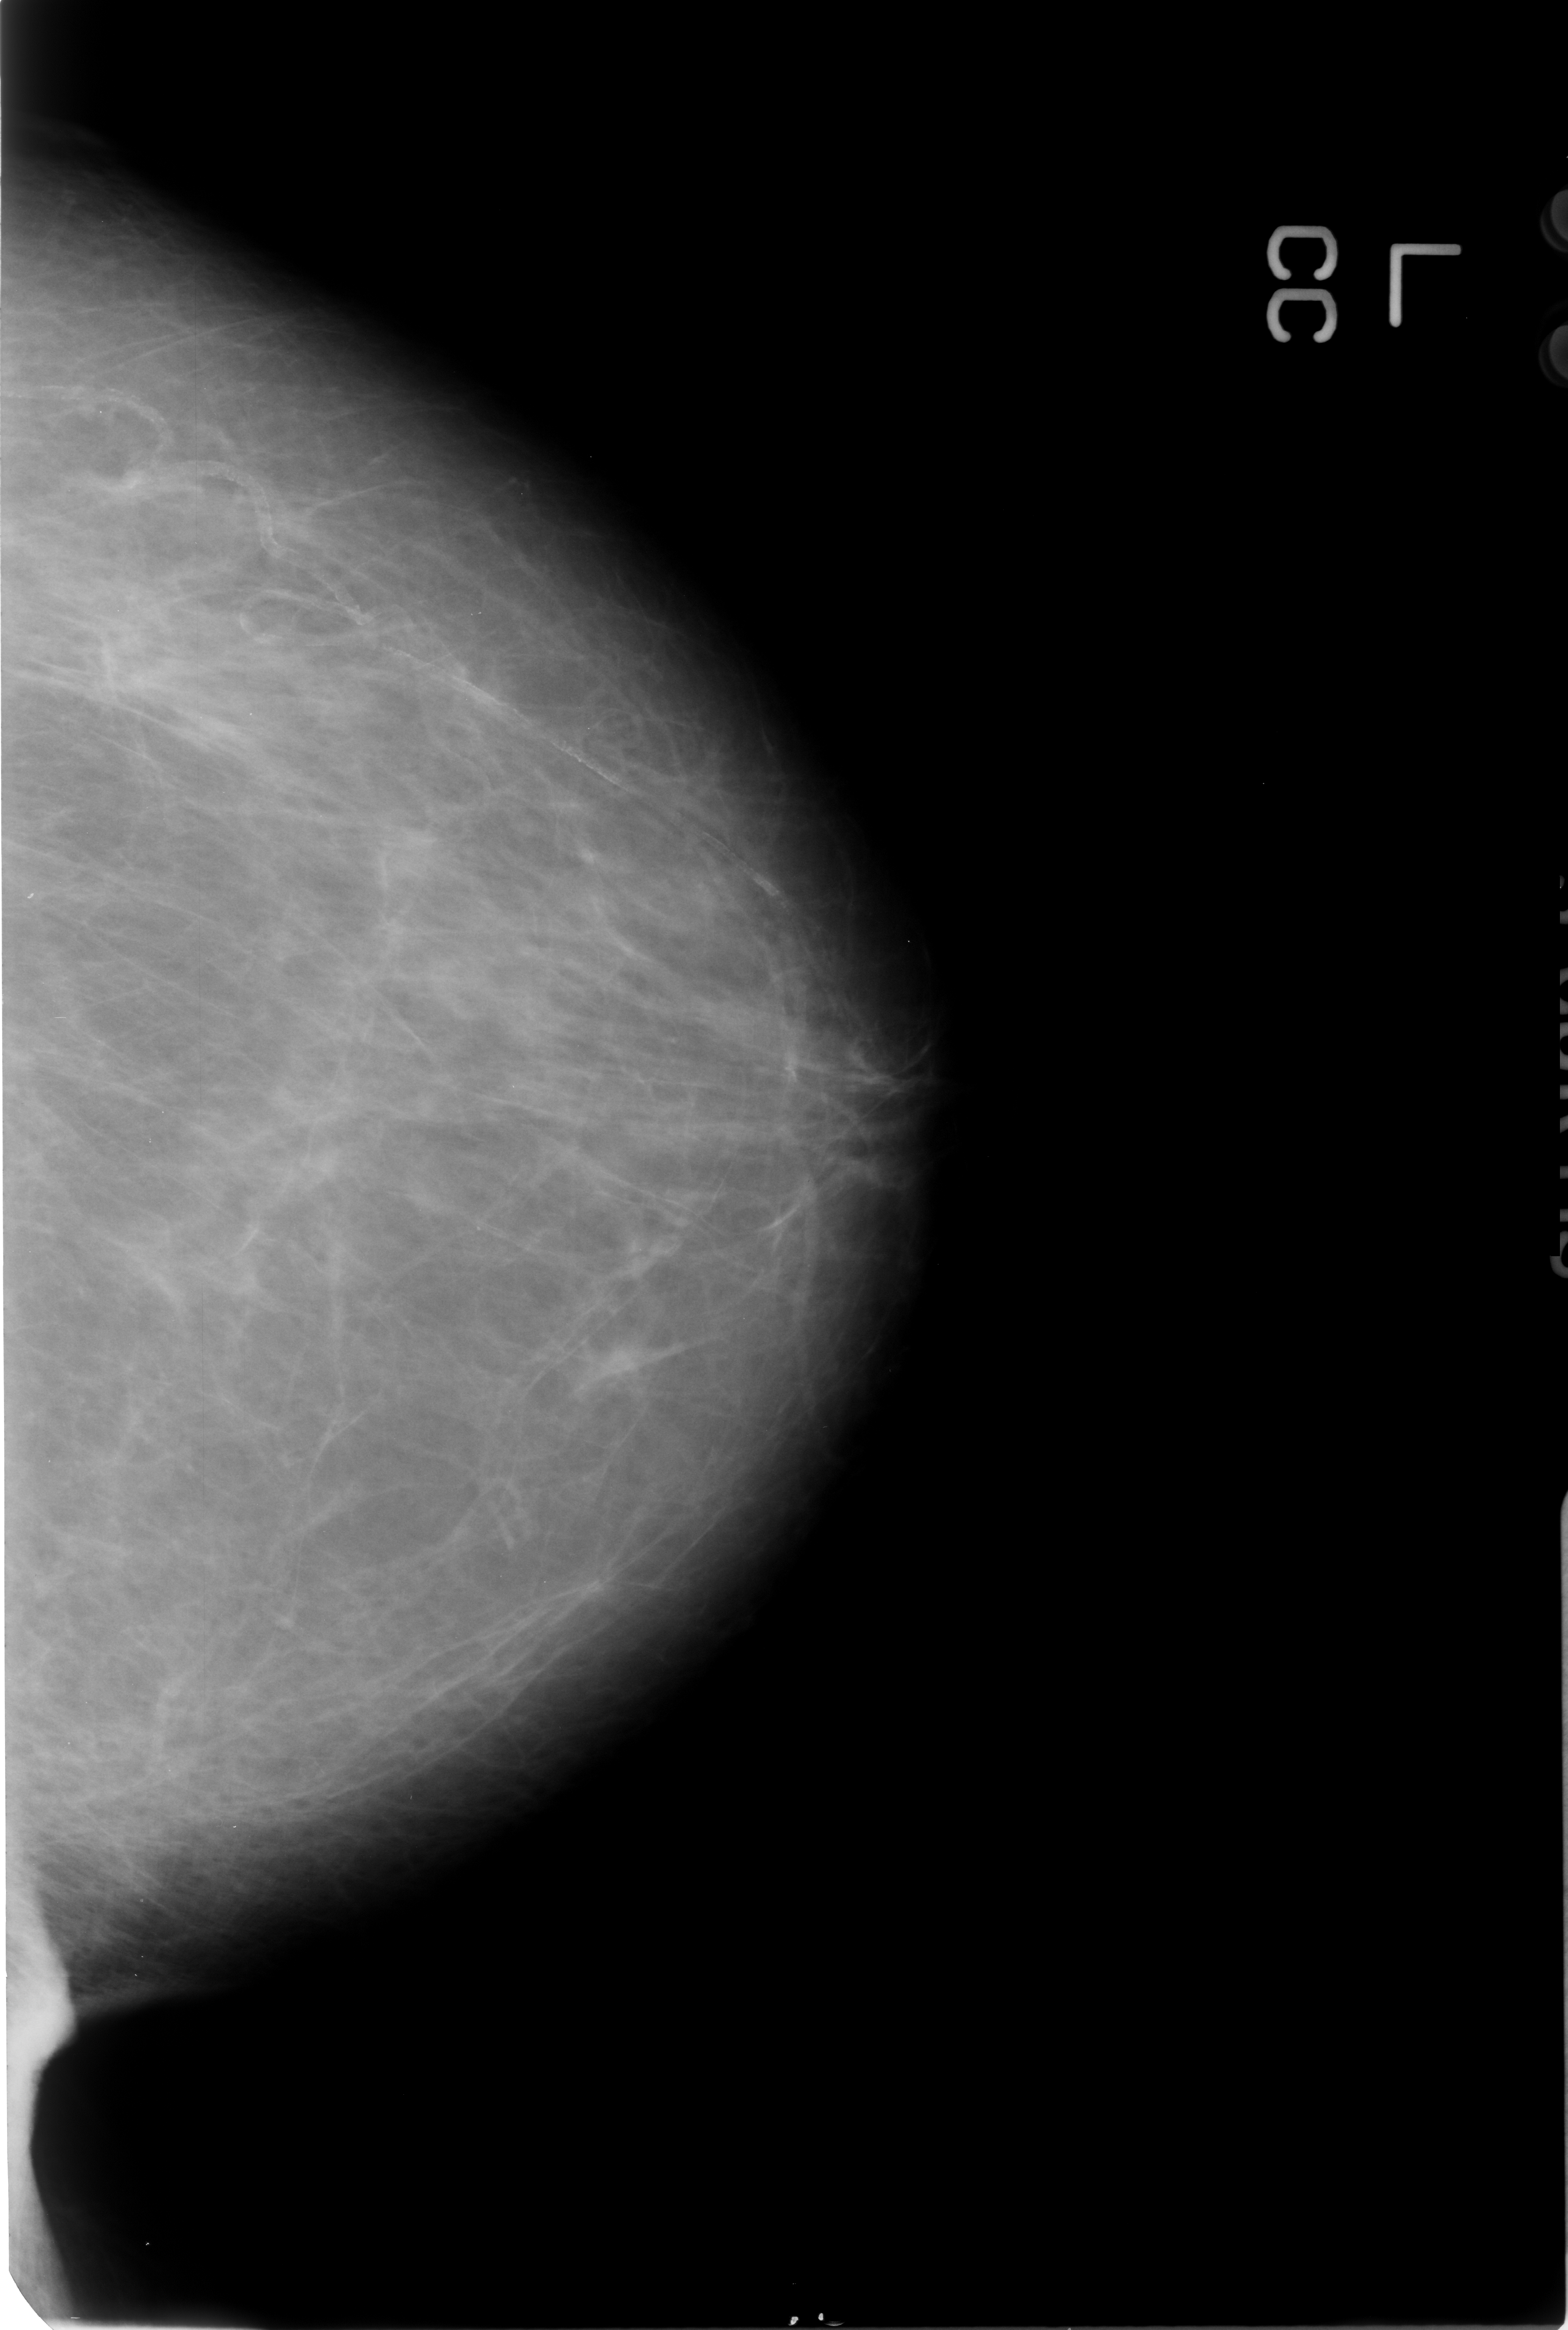
Digitized screen-film mammogram; left breast; craniocaudal (CC) view; BI-RADS breast density category 2 (scale 1–4); 1568 × 2330 image matrix.
Expert-marked regions of interest on this film, with their recorded descriptors:
- calcifications, morphology vascular; BI-RADS assessment category 2; subtlety rating 3 on a 1 (subtle) to 5 (obvious) scale; outcome (as recorded, no biopsy): benign without callback (not worked up further): bounding box [x1, y1, x2, y2] px = [64, 370, 650, 807]